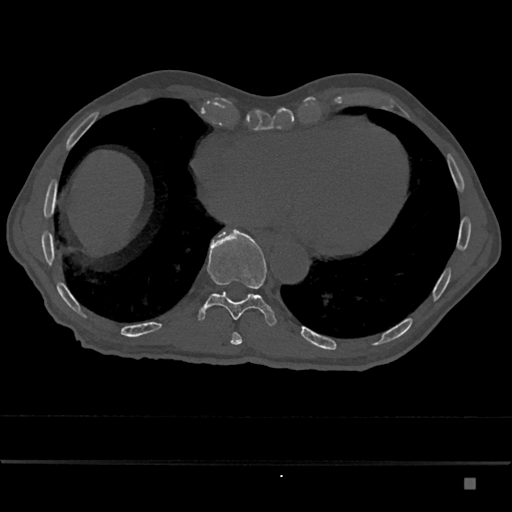
CT including the spine, one axial slice; slice 741 of 797 in the series (ordered by position); reconstruction kernel Br40s/3; bone window (W 1800 / L 400 HU); 0.5 mm slice thickness; 512 × 512 image matrix, field of view 390 × 390 mm. Male patient, age 72 years. Case-level facts recorded for this patient, not image findings: primary cancer: prostate.
Outlined on this slice (semi-automatic segmentation, software-assisted and operator-edited):
- T10 vertebra: bounding box (x1, y1, x2, y2) in pixels: (199, 229, 276, 326)
- T9 vertebra: (231, 333, 242, 345)